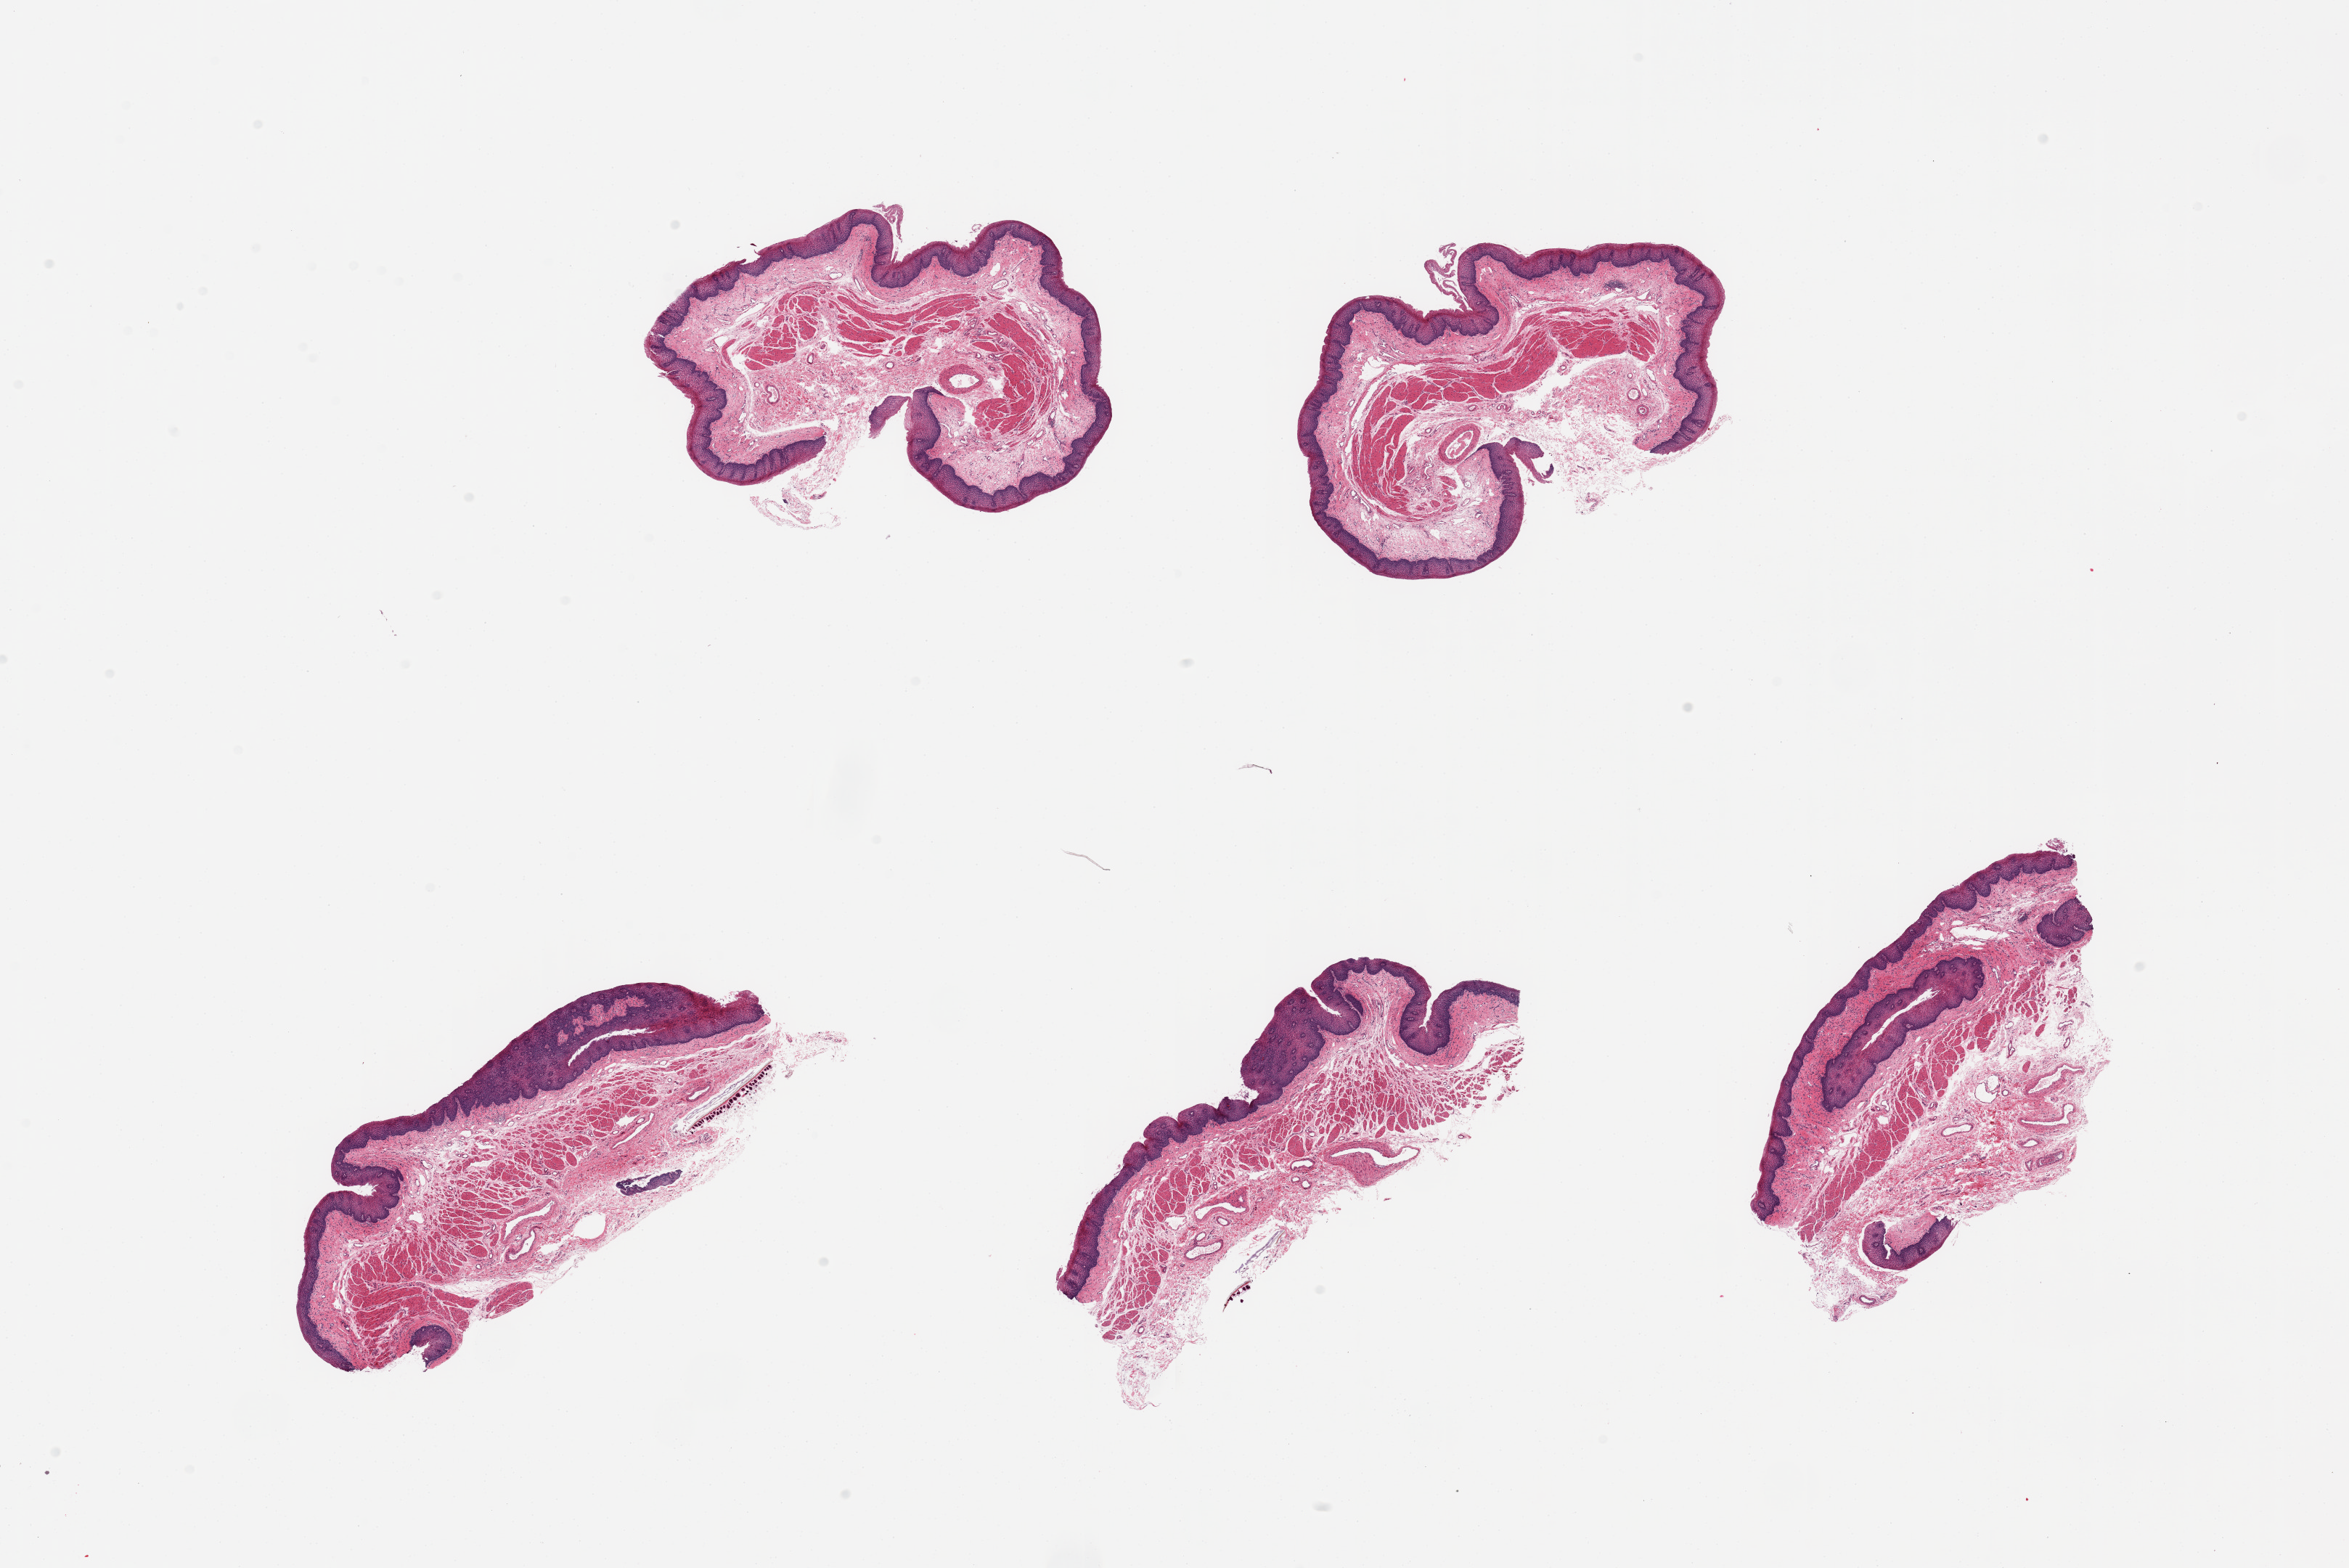
Whole-slide image, haematoxylin and eosin stain, shown as a low-resolution overview of the whole scanned area (about 25.6 x 17.1 mm), PAXgene-fixed paraffin-embedded (PFPE) section, target tissue: esophageal mucous membrane, tissue donor sample. Donor sex: female.
Pathologist's review note for this sample: 5 pieces; includes fragments of vegetable matter.